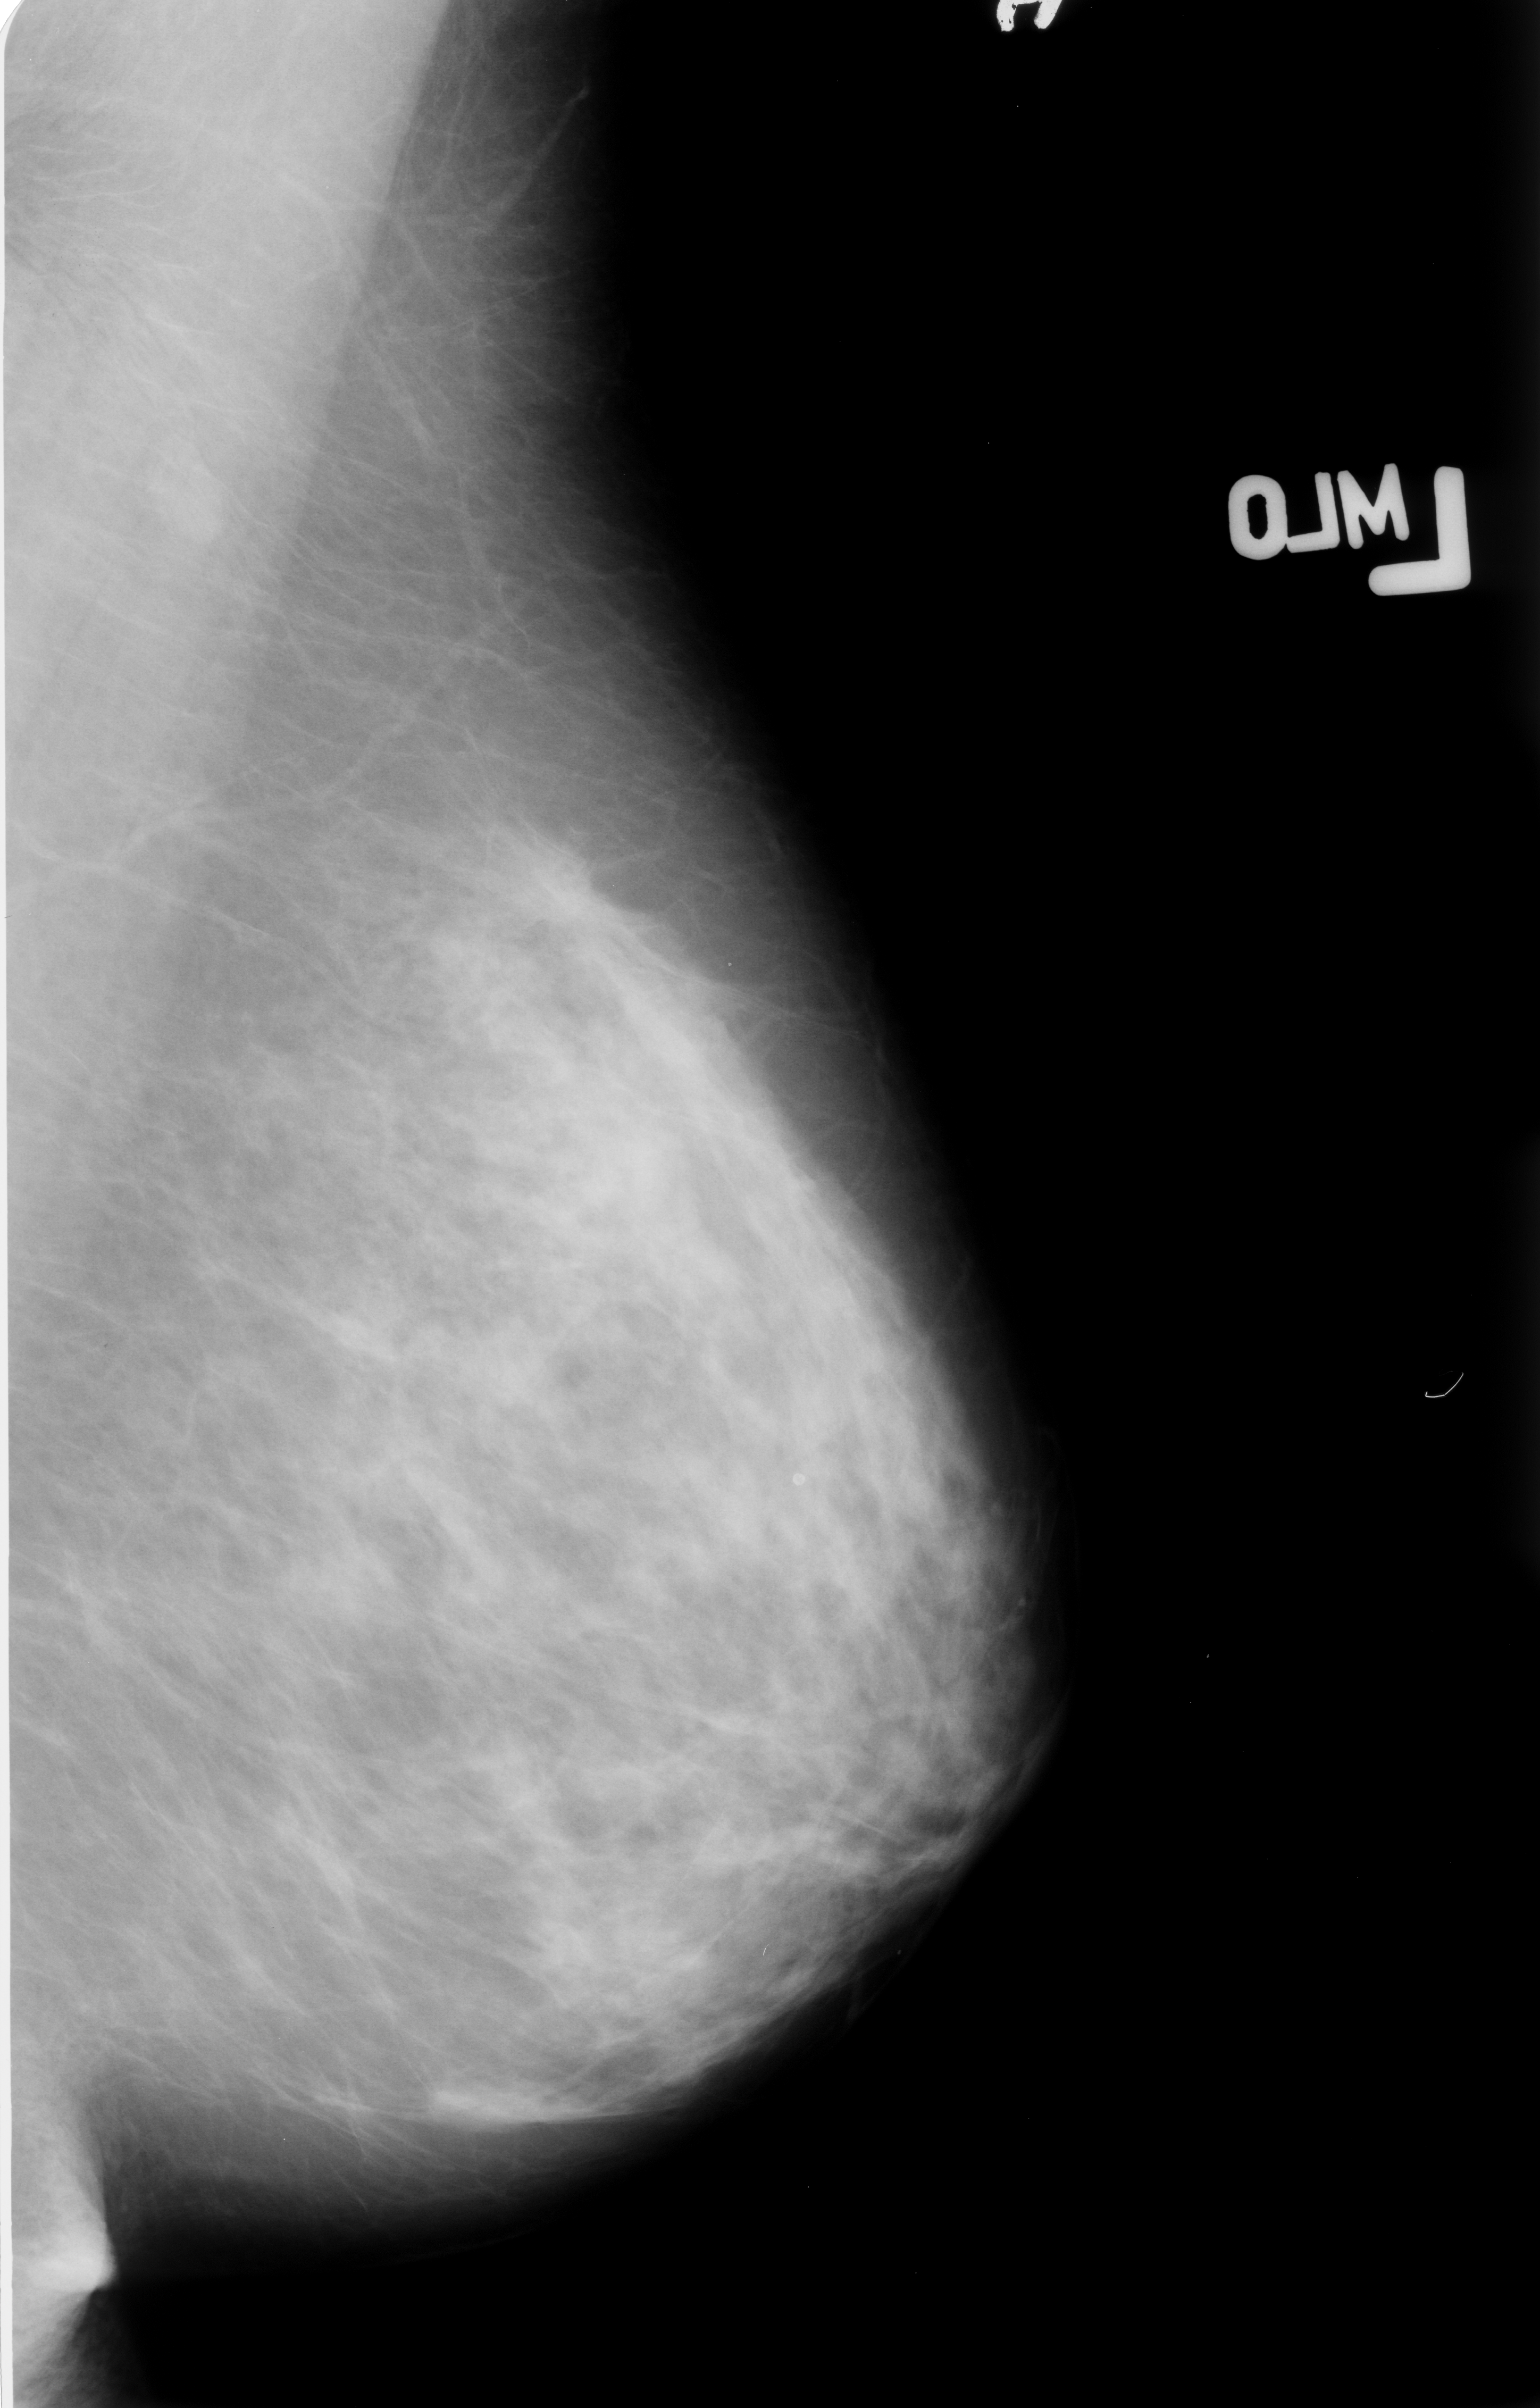
Digitized screen-film mammogram. Left breast. MLO view. Breast composition: heterogeneously dense (BI-RADS density category 3 of 4). 1540 × 2408 image matrix.
Marked abnormalities (boxes around the expert regions of interest):
- mass, shape architectural distortion, margins ill defined / spiculated; BI-RADS assessment category 4; subtlety rating 3 on a 1 (subtle) to 5 (obvious) scale; pathology (as recorded): malignant: bounding box [x1, y1, x2, y2] px = [498, 855, 623, 941]